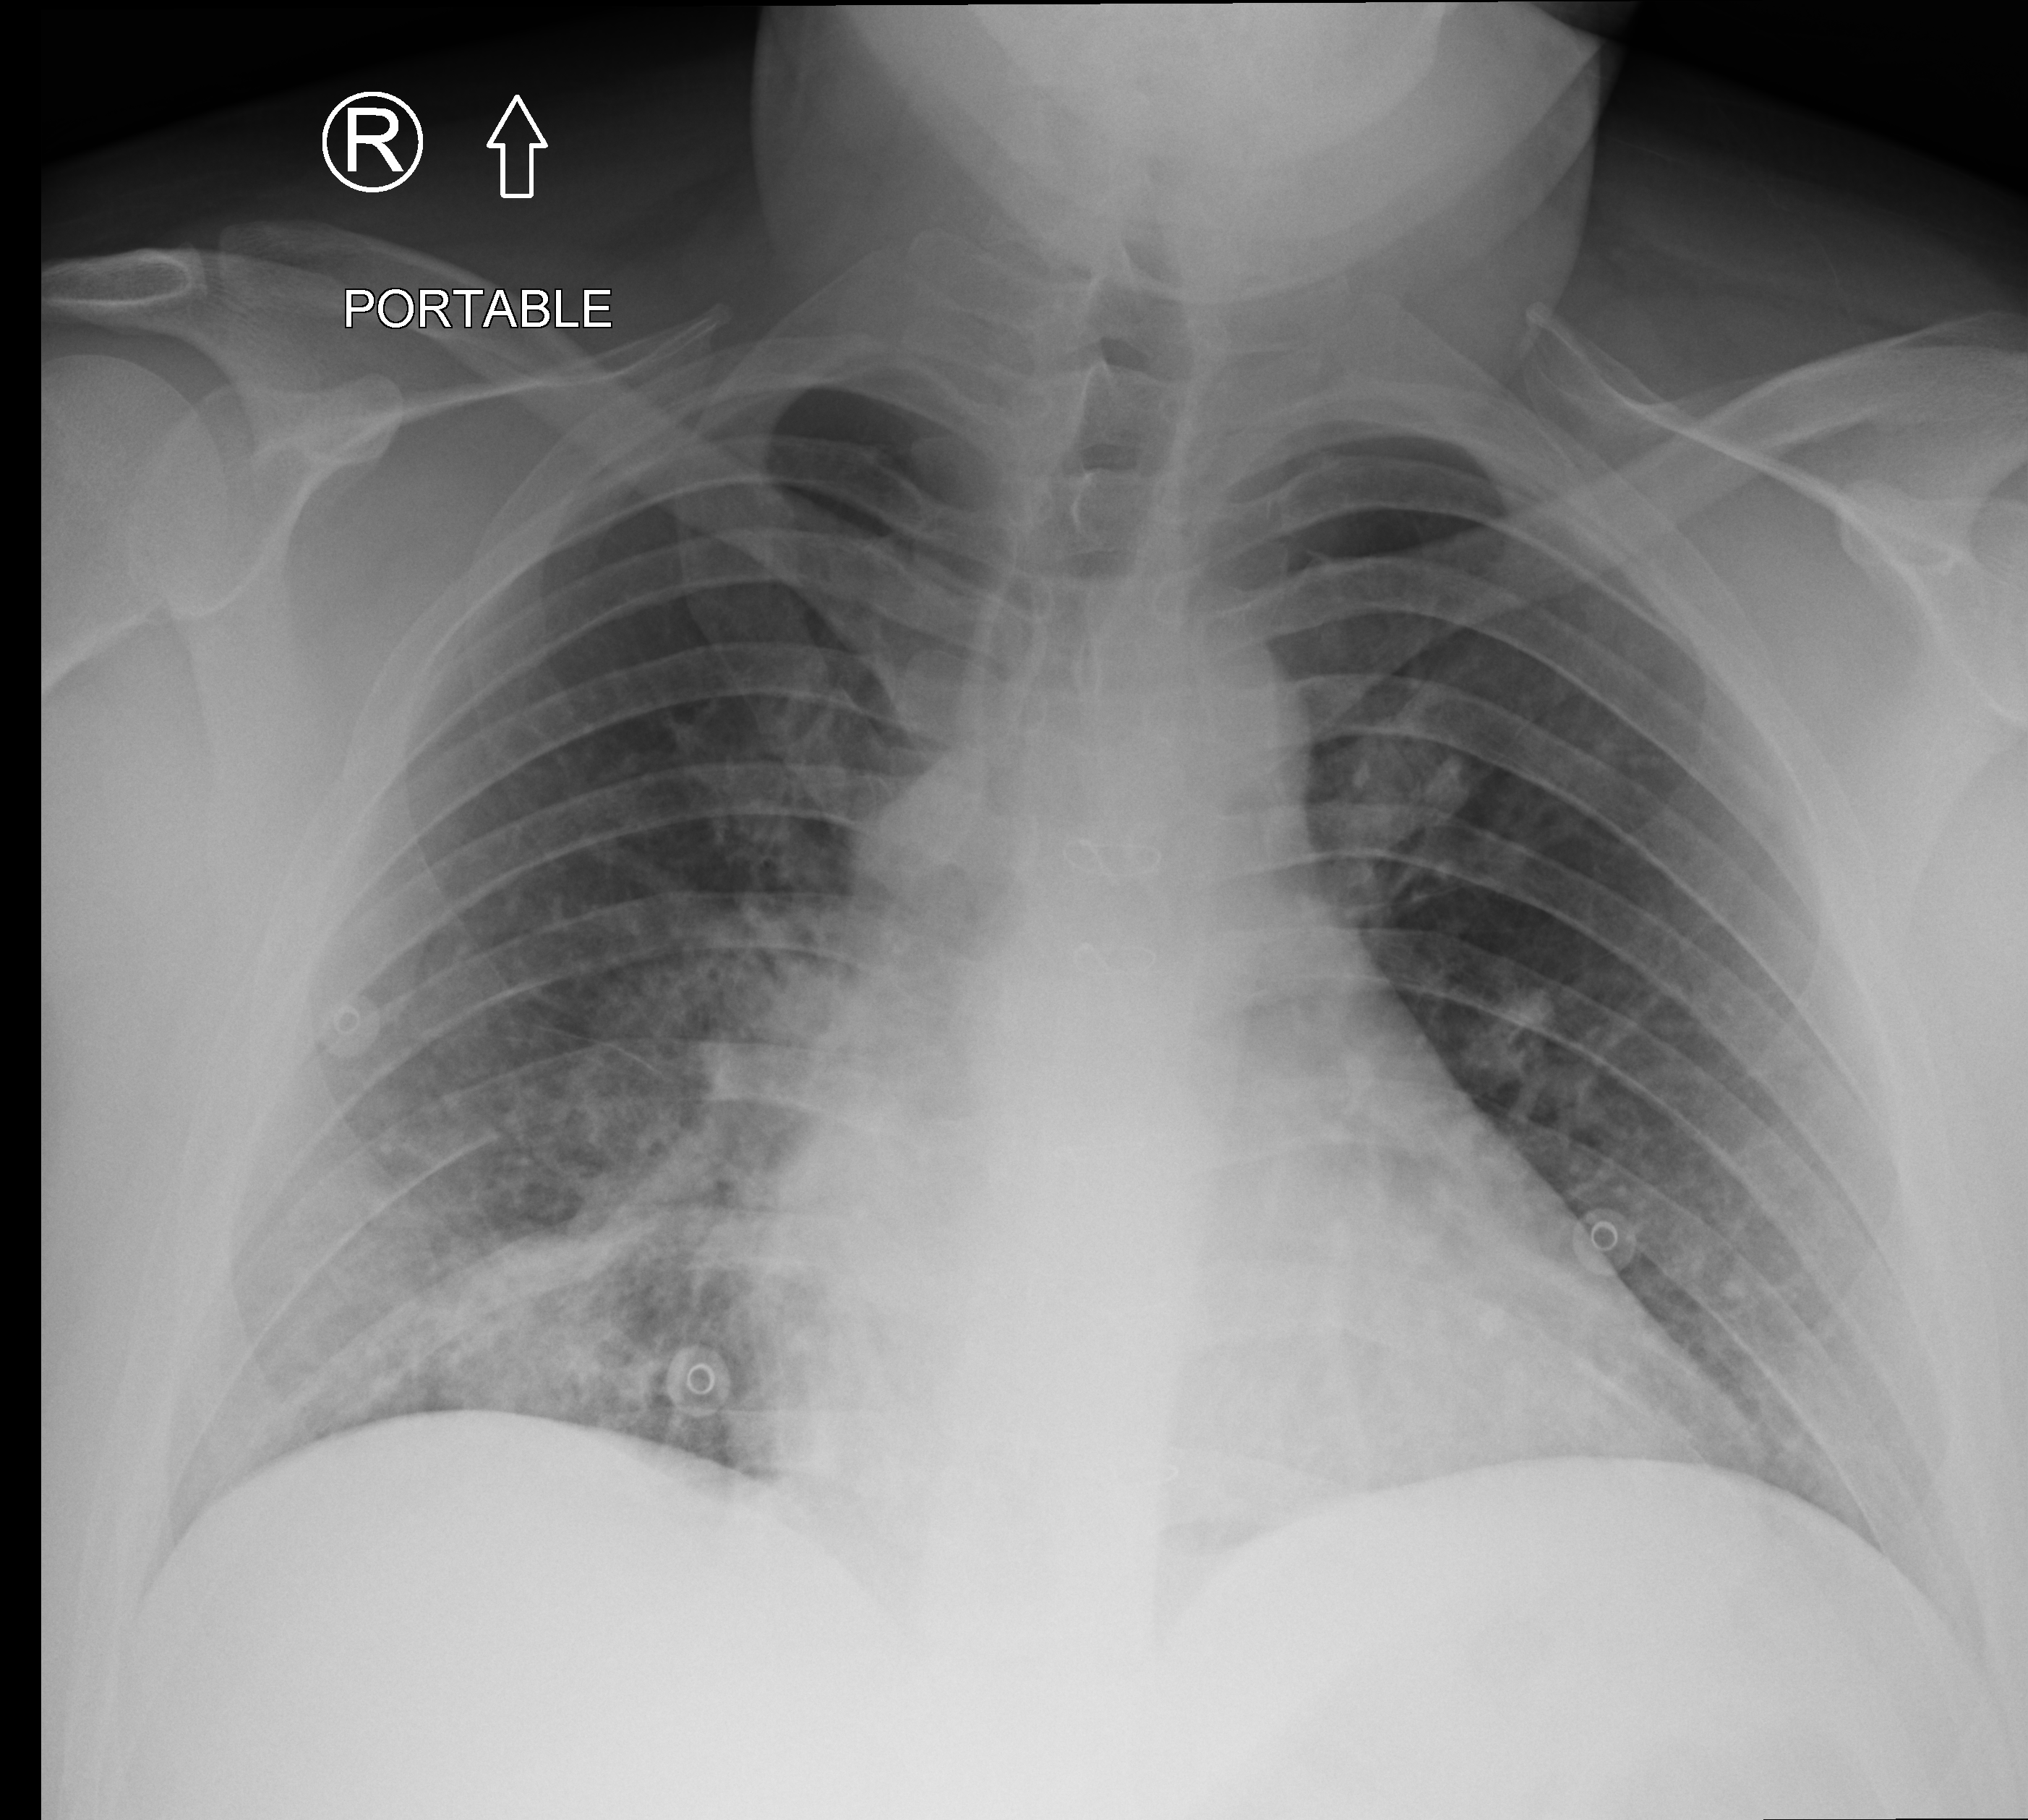
Bedside chest radiograph (computed radiography), anteroposterior (AP) projection. Patient hospitalised with COVID-19; male, aged 18–59 years.
Admission-level facts for this patient (not findings on this image; timing relative to this image not recorded):
- mechanically ventilated during this hospital stay: no